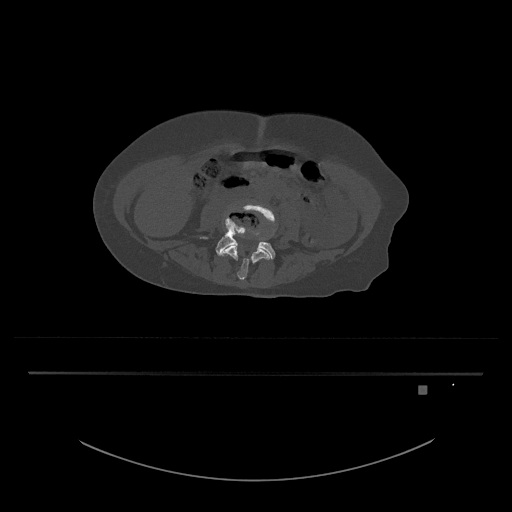
CT including the spine, one axial slice; position 334 of 797 along the scan axis; reconstruction kernel Br40s/3; 120 kVp; bone window (W 1800 / L 400 HU); 0.5 mm slice thickness; 512 × 512 image matrix, field of view 500 × 500 mm. Female patient, age 57 years. Case-level facts recorded for this patient, not image findings: primary cancer: cervical.
Outlined on this slice (semi-automatically segmented with operator editing):
- L4 vertebra: bounding box (x1, y1, x2, y2) in pixels: (220, 203, 276, 280)